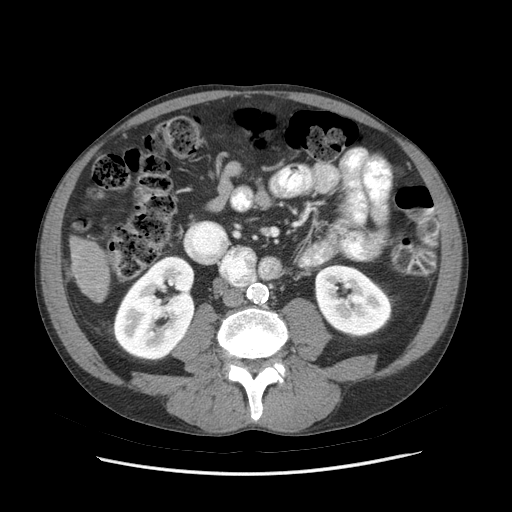
Contrast-enhanced abdominal CT (liver protocol), one axial slice; position 12 of 89 along the scan axis; soft-tissue window (W 400 / L 40 HU); 2.5 mm slice thickness; 512 × 512 image matrix, field of view 380 × 380 mm. Case-level facts recorded for this patient, not image findings: diagnosis: hepatocellular carcinoma (patient treated with transarterial chemoembolisation; whether this scan precedes or follows treatment is not stated here); TNM stage (as recorded): Stage-IIIB; Child-Pugh class: A; tumour nodularity: multinodular.
Annotated regions visible in this slice (semi-automatically segmented with operator editing):
- liver parenchyma outside the tumour (the mass and vessels are separate outlines, so this box may not span the whole liver): bounding box <70,236,108,300> (left, top, right, bottom; pixels)